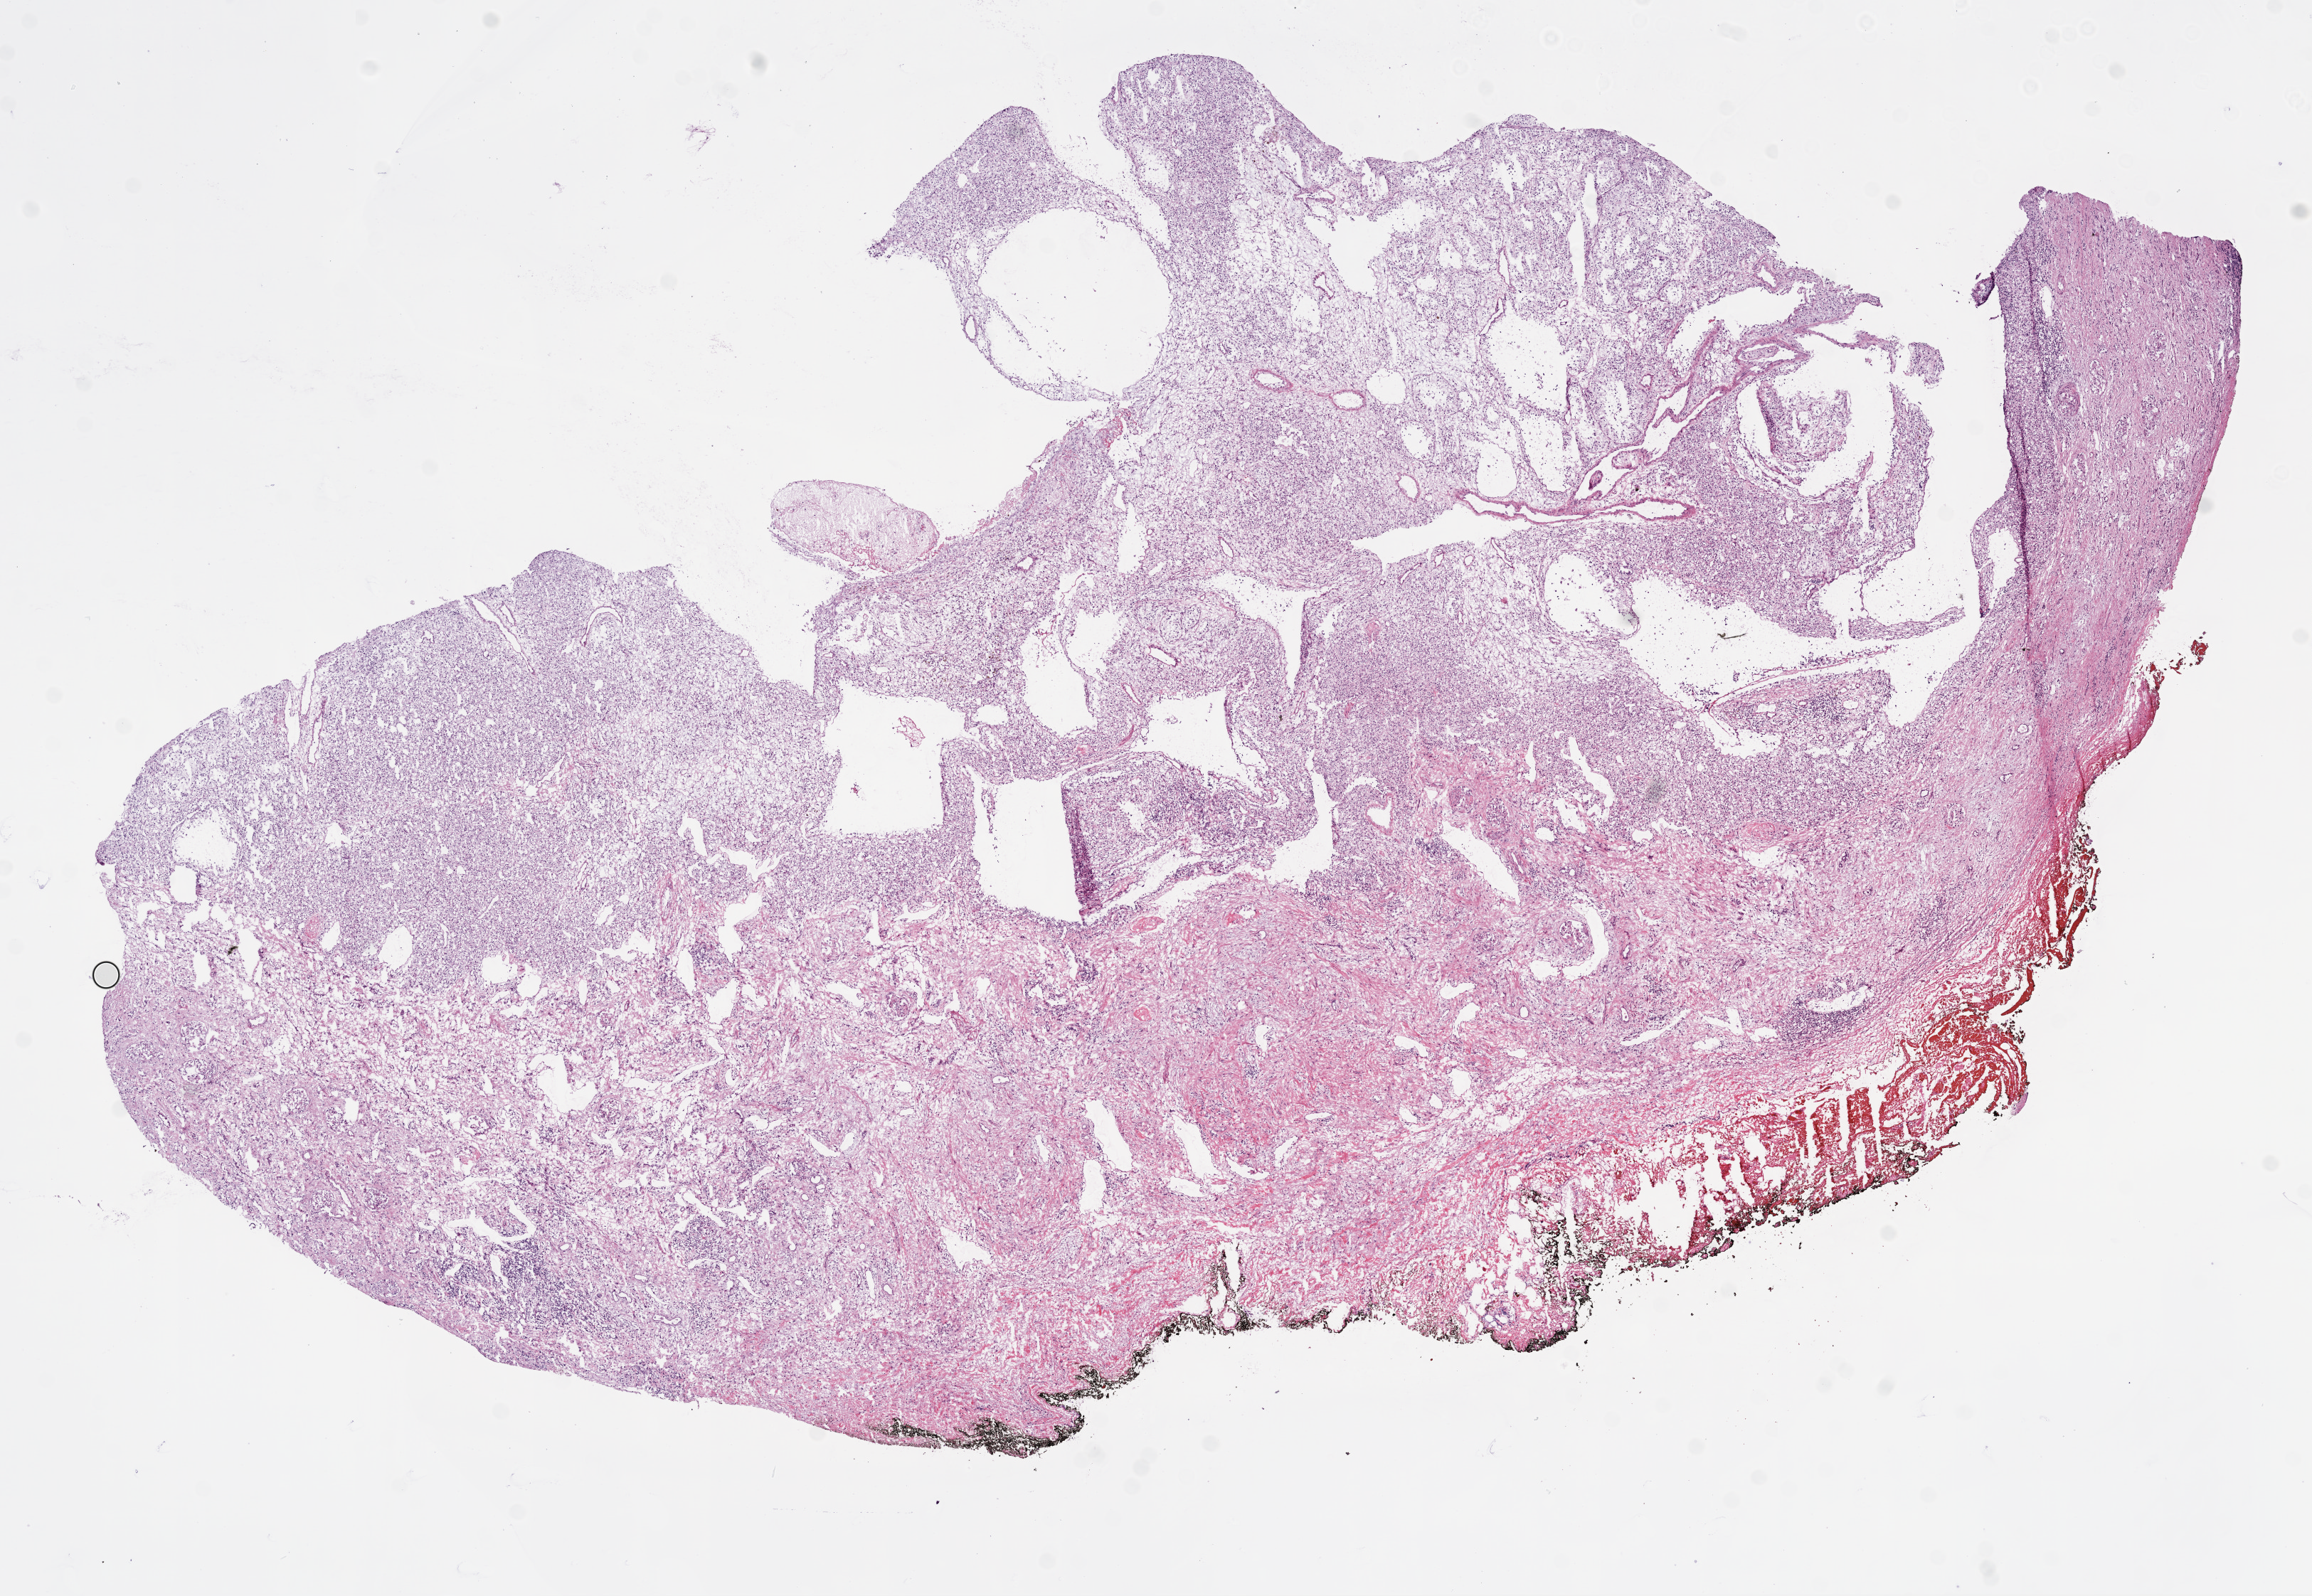
H&E whole-slide image, low-resolution overview of the scanned area, about 13.0 x 9.0 mm (from a 20x scan), frozen section from the bottom of the tissue portion, sample: primary tumour, kidney. Male, age 42 years at initial diagnosis. Histologic grade: G3 (poorly differentiated). Slide review estimates, as recorded: tumour cells 61%, tumour nuclei 70%, normal cells 0%, stromal cells 39%, necrosis 0%.
AJCC pathologic stage: I. Histologic diagnosis: Clear cell adenocarcinoma, NOS. Laterality: left.